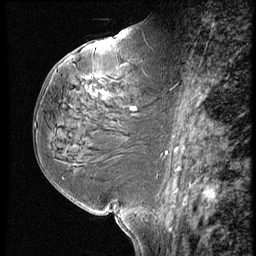
Breast MRI (dynamic contrast-enhanced), one sagittal slice. Slice 34 of 60 in the series (ordered by position). 3 images stored at this slice position (order not interpretable as contrast timing). 1.5 T. TE 4.2 ms, TR 9 ms. 2.5 mm slice thickness. 256 × 256 image matrix, field of view 180 × 180 mm. Patient: female, 59 years. From the clinical record (not read from this slice): setting: breast cancer imaged before/during neoadjuvant chemotherapy; receptor status: HER2-positive.
Structures marked on this image (semi-automatic segmentation, software-assisted and operator-edited):
- analysis volume of interest (the breast-tissue region the enhancement analysis was run in; not a lesion): bounding box [x1, y1, x2, y2] px = [78, 61, 161, 125]
- tumour enhancement mask (voxels above the 140 % enhancement threshold inside the analysis volume of interest): [132, 109, 136, 111]